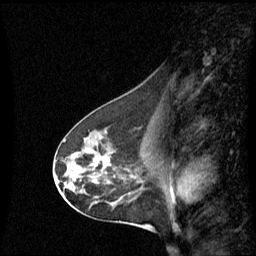
Breast MRI (dynamic contrast-enhanced), one sagittal slice; slice 32 of 60 in the series (ordered by position); dynamic contrast-enhanced series, image 2 of 3 at this slice position (ordered by acquisition); 1.5 T; TE 4.2 ms, TR 8.4 ms; 2.2 mm slice thickness; 256 × 256 image matrix. Patient: female, 45 years. From the clinical record (not read from this slice): setting: breast cancer imaged before/during neoadjuvant chemotherapy; receptor status: HR-positive, HER2-negative.
Annotated regions visible in this slice (semi-automatically segmented with operator editing):
- analysis volume of interest (the breast-tissue region the enhancement analysis was run in; not a lesion): bounding box (x1, y1, x2, y2) in pixels: (60, 126, 149, 215)
- tumour enhancement mask (voxels above the 70 % enhancement threshold inside the analysis volume of interest): (94, 132, 106, 163)